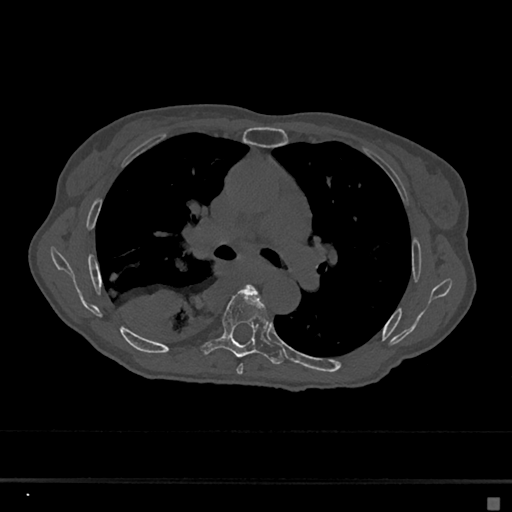
CT including the spine, one axial slice; position 426 of 797 along the scan axis; 120 kVp; bone window (W 1800 / L 400 HU); 0.5 mm slice thickness; 512 × 512 image matrix, field of view 360 × 360 mm. Female patient, age 68 years. Case-level facts recorded for this patient, not image findings: primary cancer: renal.
Annotated regions visible in this slice (semi-automatic segmentation, software-assisted and operator-edited):
- T5 vertebra: bounding box (x1, y1, x2, y2) in pixels: (236, 285, 260, 375)
- T6 vertebra: (203, 287, 284, 365)